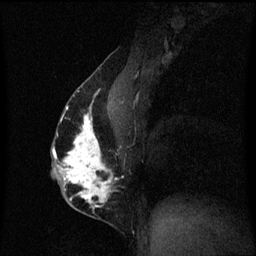
Breast MRI (dynamic contrast-enhanced), one sagittal slice; position 33 of 60 along the scan axis; dynamic contrast-enhanced series, image 2 of 3 at this slice position (ordered by acquisition); 1.5 T; TE 4.2 ms, TR 8.4 ms; 256 × 256 image matrix, field of view 200 × 200 mm. Female patient, age 40 years.
Annotated regions visible in this slice (semi-automatic segmentation, software-assisted and operator-edited):
- analysis volume of interest (the breast-tissue region the enhancement analysis was run in; not a lesion): bounding box <52,84,123,211> (left, top, right, bottom; pixels)
- tumour enhancement mask (voxels above the 70 % enhancement threshold inside the analysis volume of interest): <53,90,114,209>